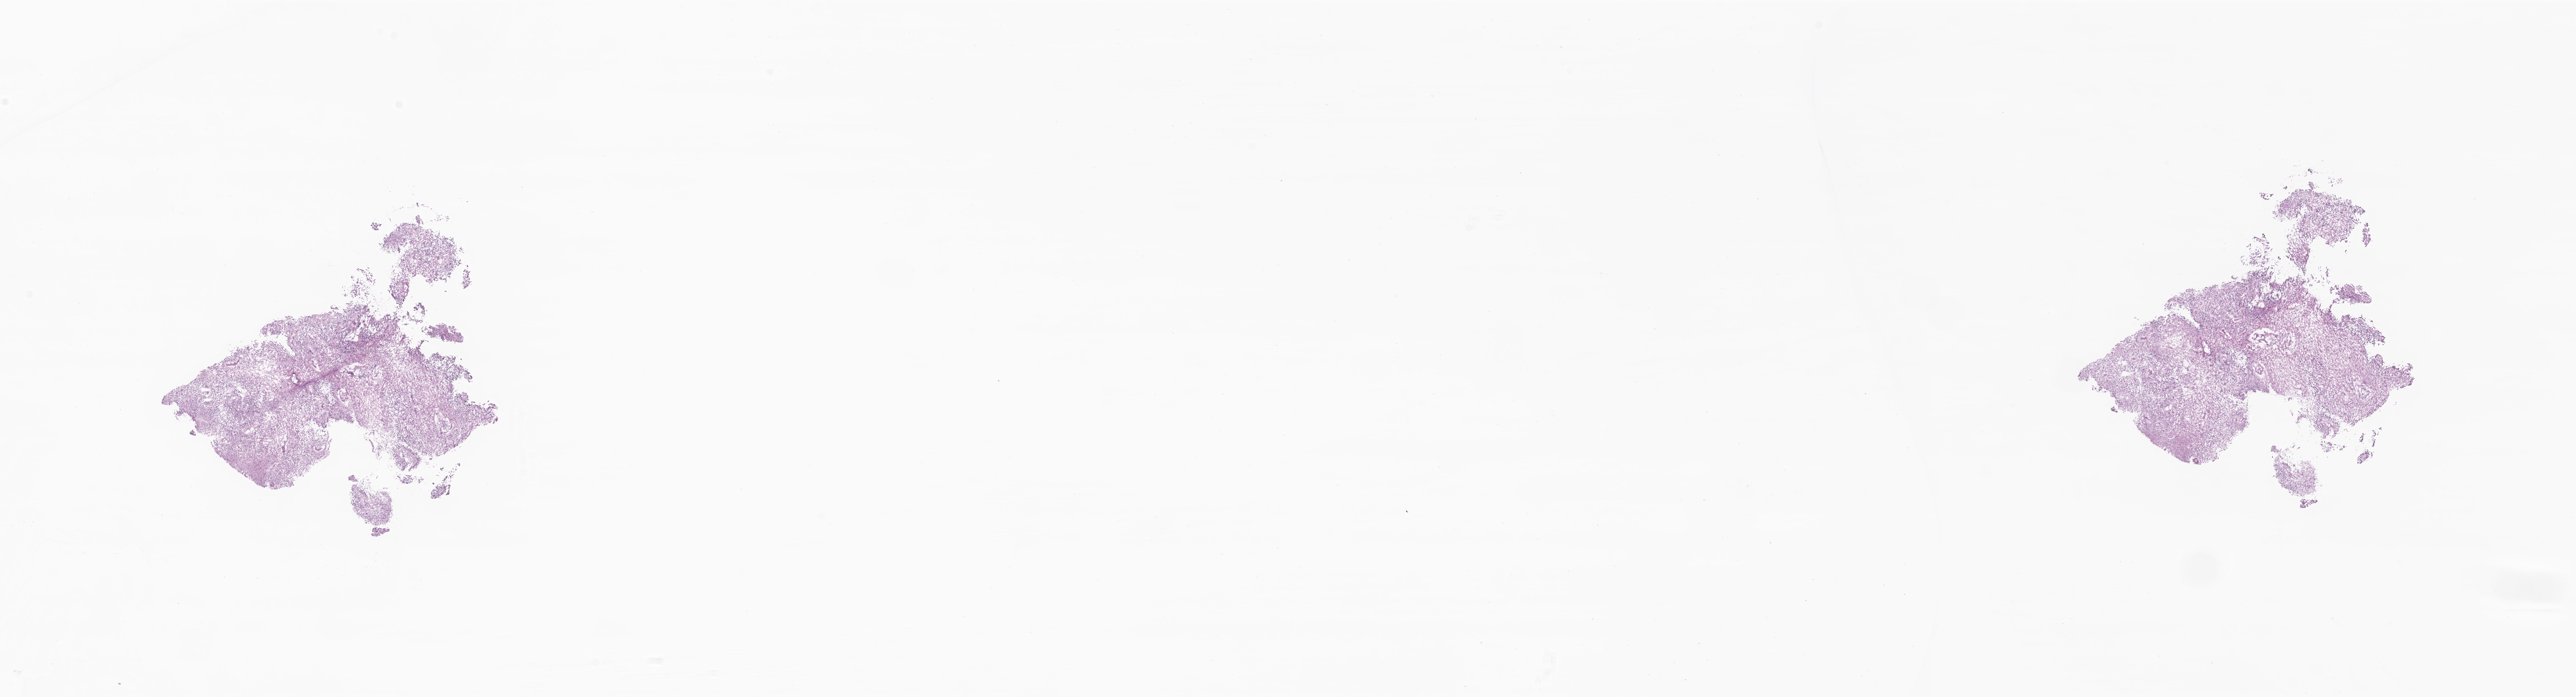
H&E whole-slide image of tumor tissue from the brain, shown as a low-resolution overview of the whole scanned area (about 30.6 x 8.3 mm); cryosection (OCT / tissue freezing medium). Patient female; age 685 days (about 1.9 years).
Diagnosis: Ependymoma, NOS.